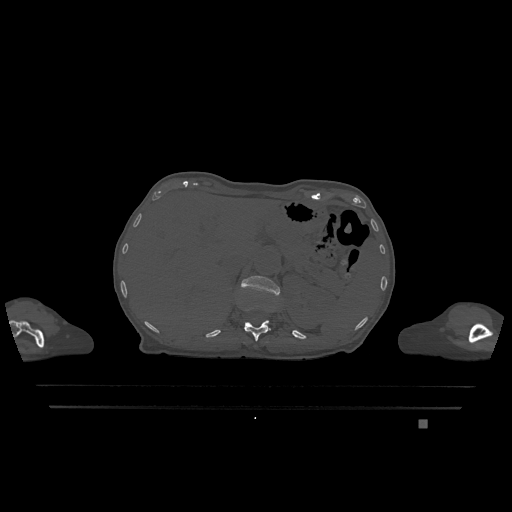
CT including the spine, one axial slice. Slice 517 of 1317 in the series (ordered by position). Bone window (W 1800 / L 400 HU). 0.5 mm slice thickness. 512 × 512 image matrix, field of view 500 × 500 mm. Female patient, age 74 years. Case-level facts recorded for this patient, not image findings: primary cancer: lung; vertebrae with lytic lesions (as recorded): T1, T4, T5, T6, L4, L5.
Annotated regions visible in this slice (semi-automatic segmentation, software-assisted and operator-edited):
- L1 vertebra: bounding box <241,276,280,296> (left, top, right, bottom; pixels)
- T12 vertebra: <244,305,270,341>